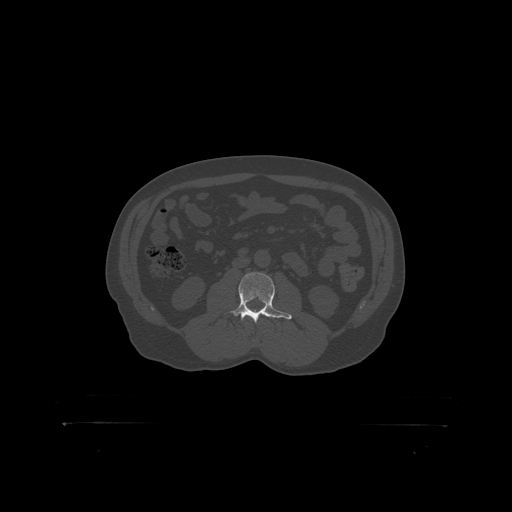
CT including the spine, one axial slice. Slice 268 of 399 in the series (ordered by position). Reconstruction kernel STANDARD. 120 kVp. Bone window (W 1800 / L 400 HU). 1.25 mm slice thickness. 512 × 512 image matrix, field of view 650 × 650 mm. Male patient, age 46 years. From the clinical record (not read from this slice): primary cancer: skin.
Annotated regions visible in this slice (semi-automatic segmentation, software-assisted and operator-edited):
- L3 vertebra: bounding box [x1, y1, x2, y2] px = [230, 273, 282, 319]